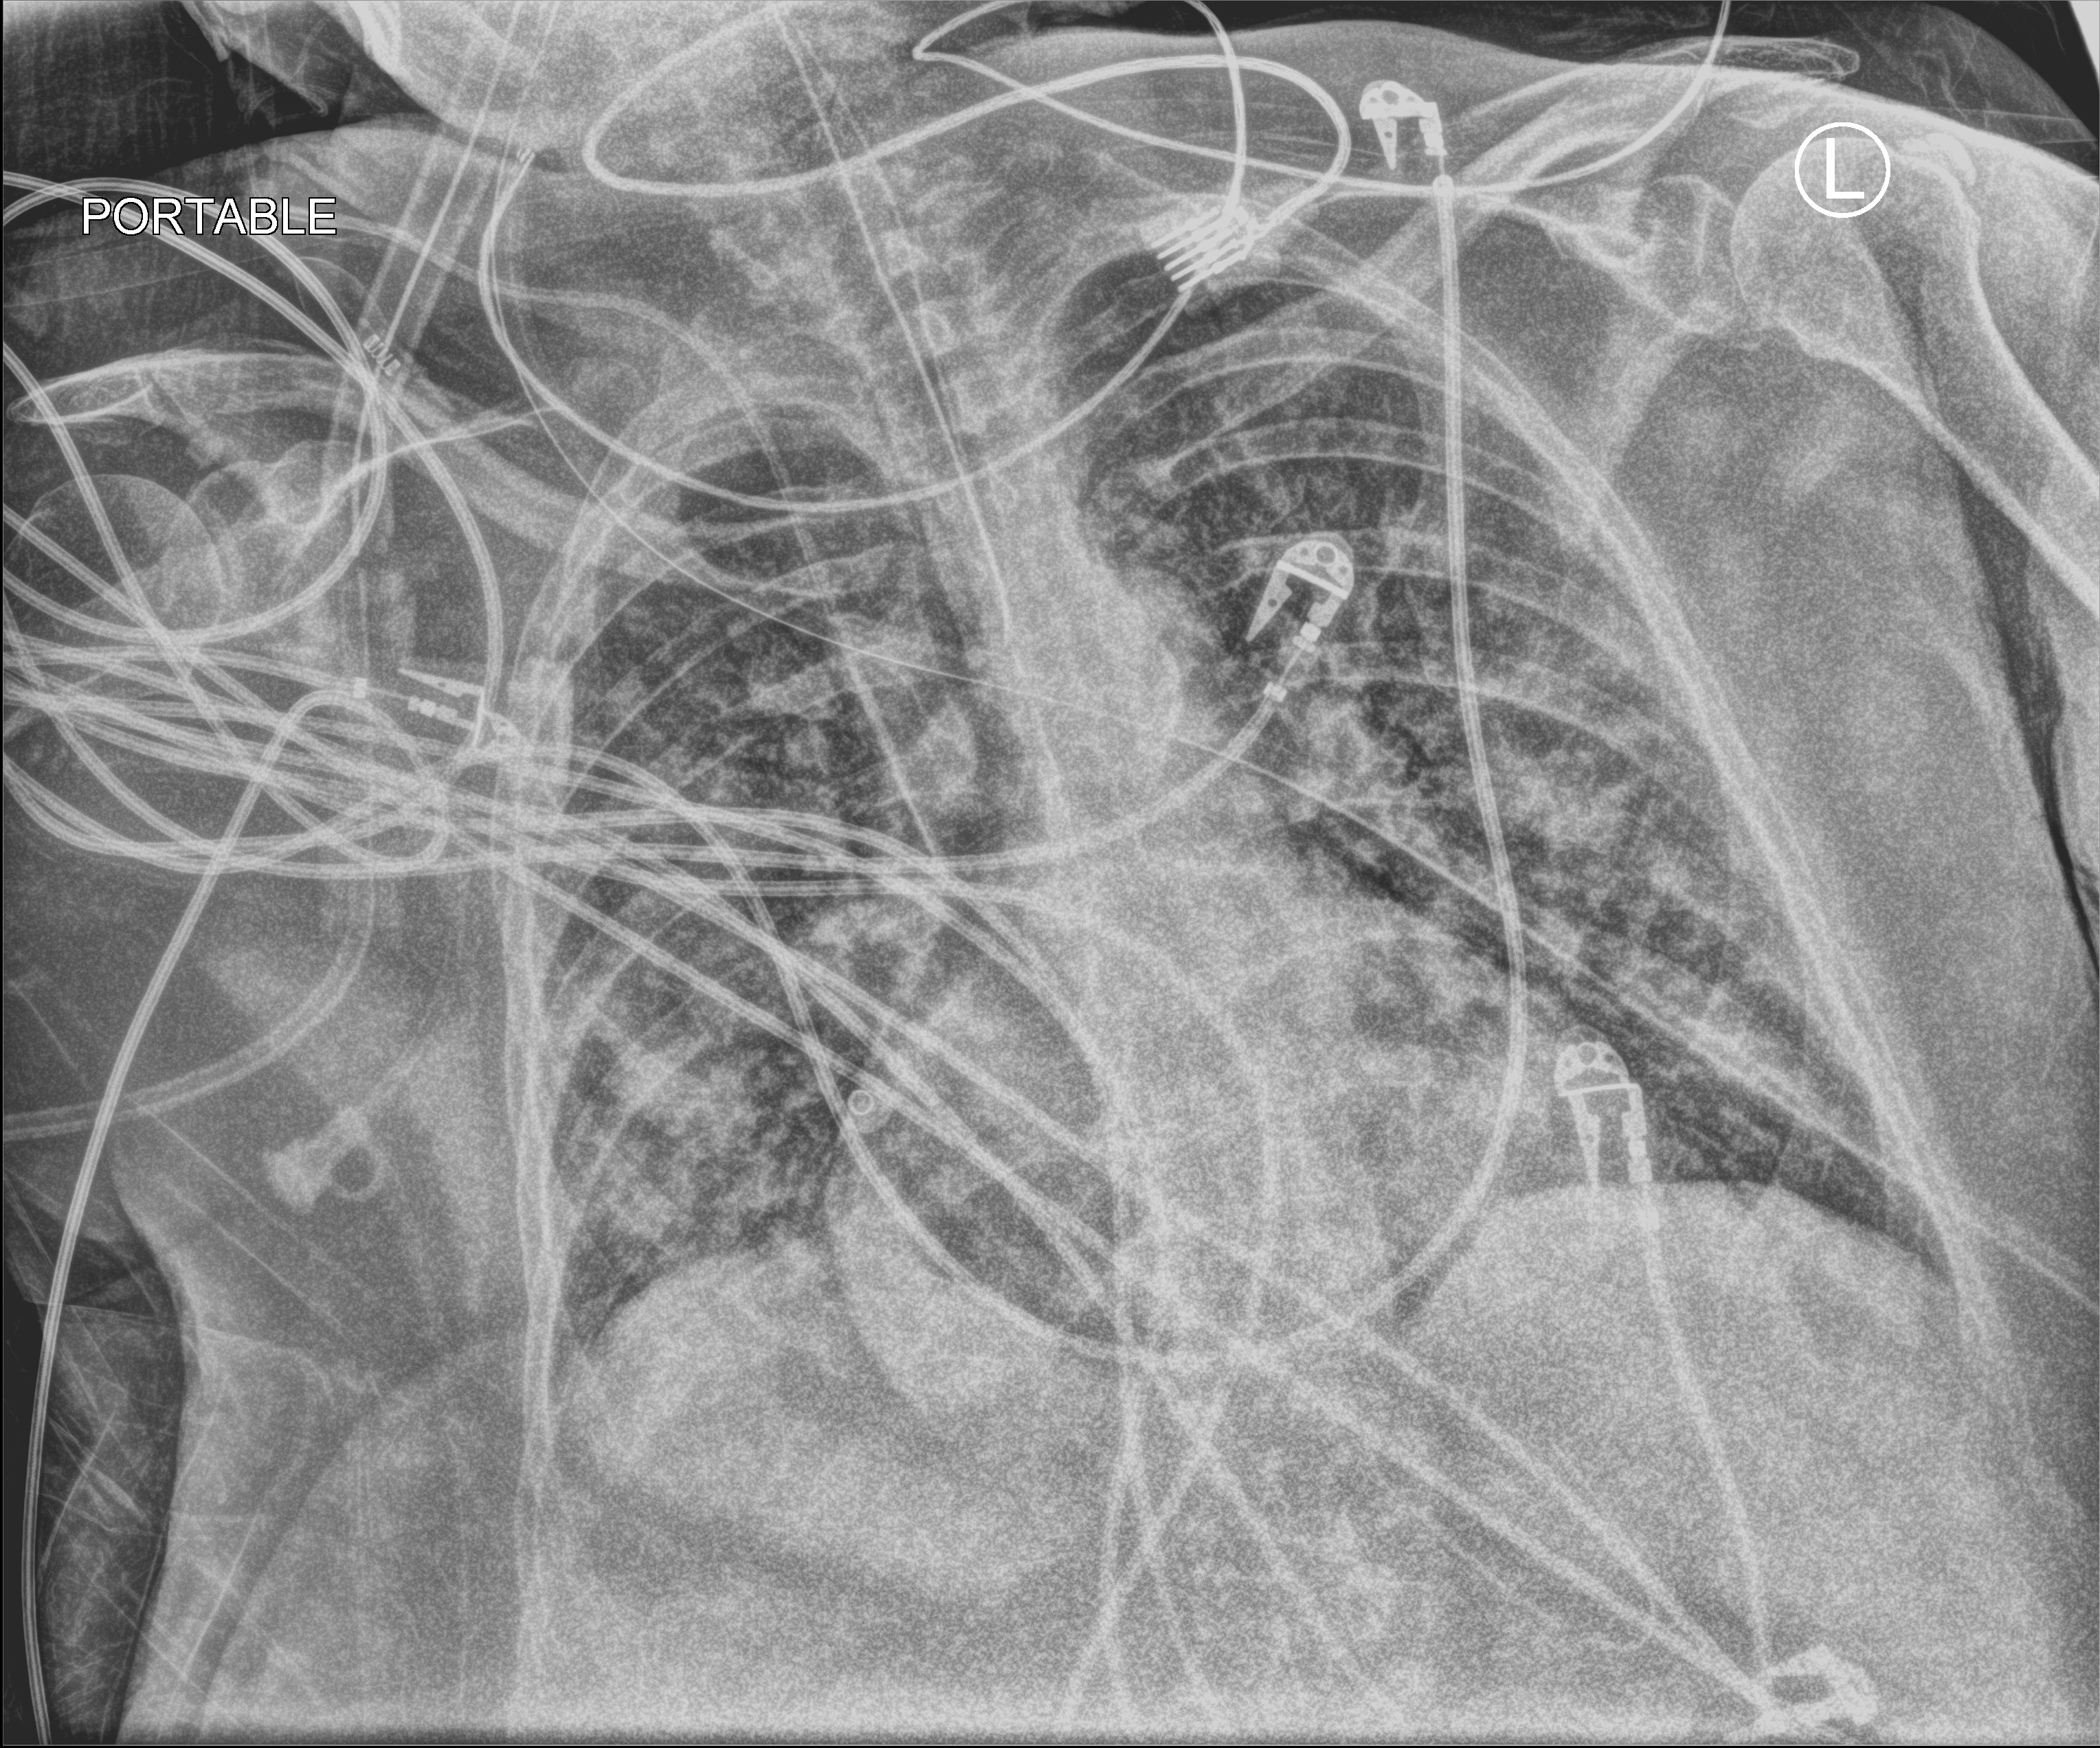
Portable chest radiograph, anteroposterior (AP) projection. Female patient hospitalised with COVID-19, age 75–90 years.
Hospital-stay facts (about this admission, not read from this image; timing relative to this image not recorded): admitted to intensive care during this hospital stay: yes.